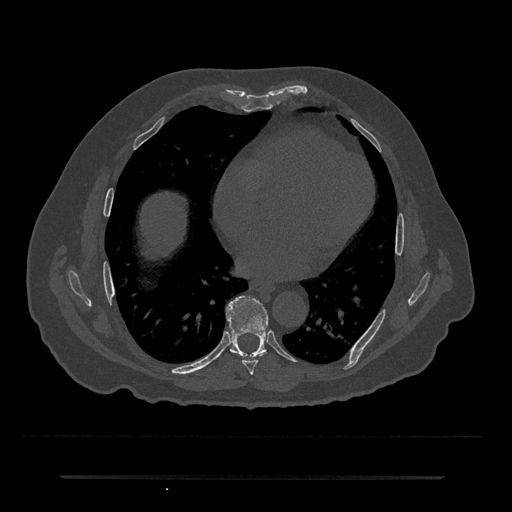
CT including the spine, one axial slice. Slice 358 of 797 in the series (ordered by position). Reconstruction kernel Br40s/3. Bone window (W 1800 / L 400 HU). 0.5 mm slice thickness. 512 × 512 image matrix, field of view 437 × 437 mm. Patient: male, 69 years. Case-level facts recorded for this patient, not image findings: primary cancer: prostate.
Outlined on this slice (semi-automatic segmentation, software-assisted and operator-edited):
- T7 vertebra: box from (x=242, y=352) to (x=266, y=375) px
- T8 vertebra: (x=226, y=296)–(x=268, y=358)